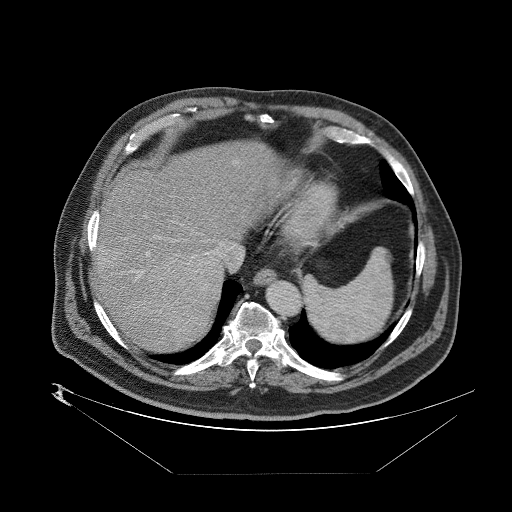
Contrast-enhanced abdominal CT (liver protocol), one axial slice; position 69 of 89 along the scan axis; reconstruction kernel STANDARD; 140 kVp; one of 2 acquisitions stored at this slice position; soft-tissue window (W 400 / L 40 HU); 2.5 mm slice thickness; 512 × 512 image matrix. Case-level facts recorded for this patient, not image findings: diagnosis: hepatocellular carcinoma (patient treated with transarterial chemoembolisation; whether this scan precedes or follows treatment is not stated here); TNM stage (as recorded): Stage-II; Child-Pugh class: B.
Outlined on this slice (semi-automatically segmented with operator editing):
- abdominal aorta: bounding box <266,282,300,316> (left, top, right, bottom; pixels)
- liver parenchyma outside the tumour (the mass and vessels are separate outlines, so this box may not span the whole liver): <90,138,290,336>
- mass: <153,253,220,314>
- liver vessels: <92,159,286,321>